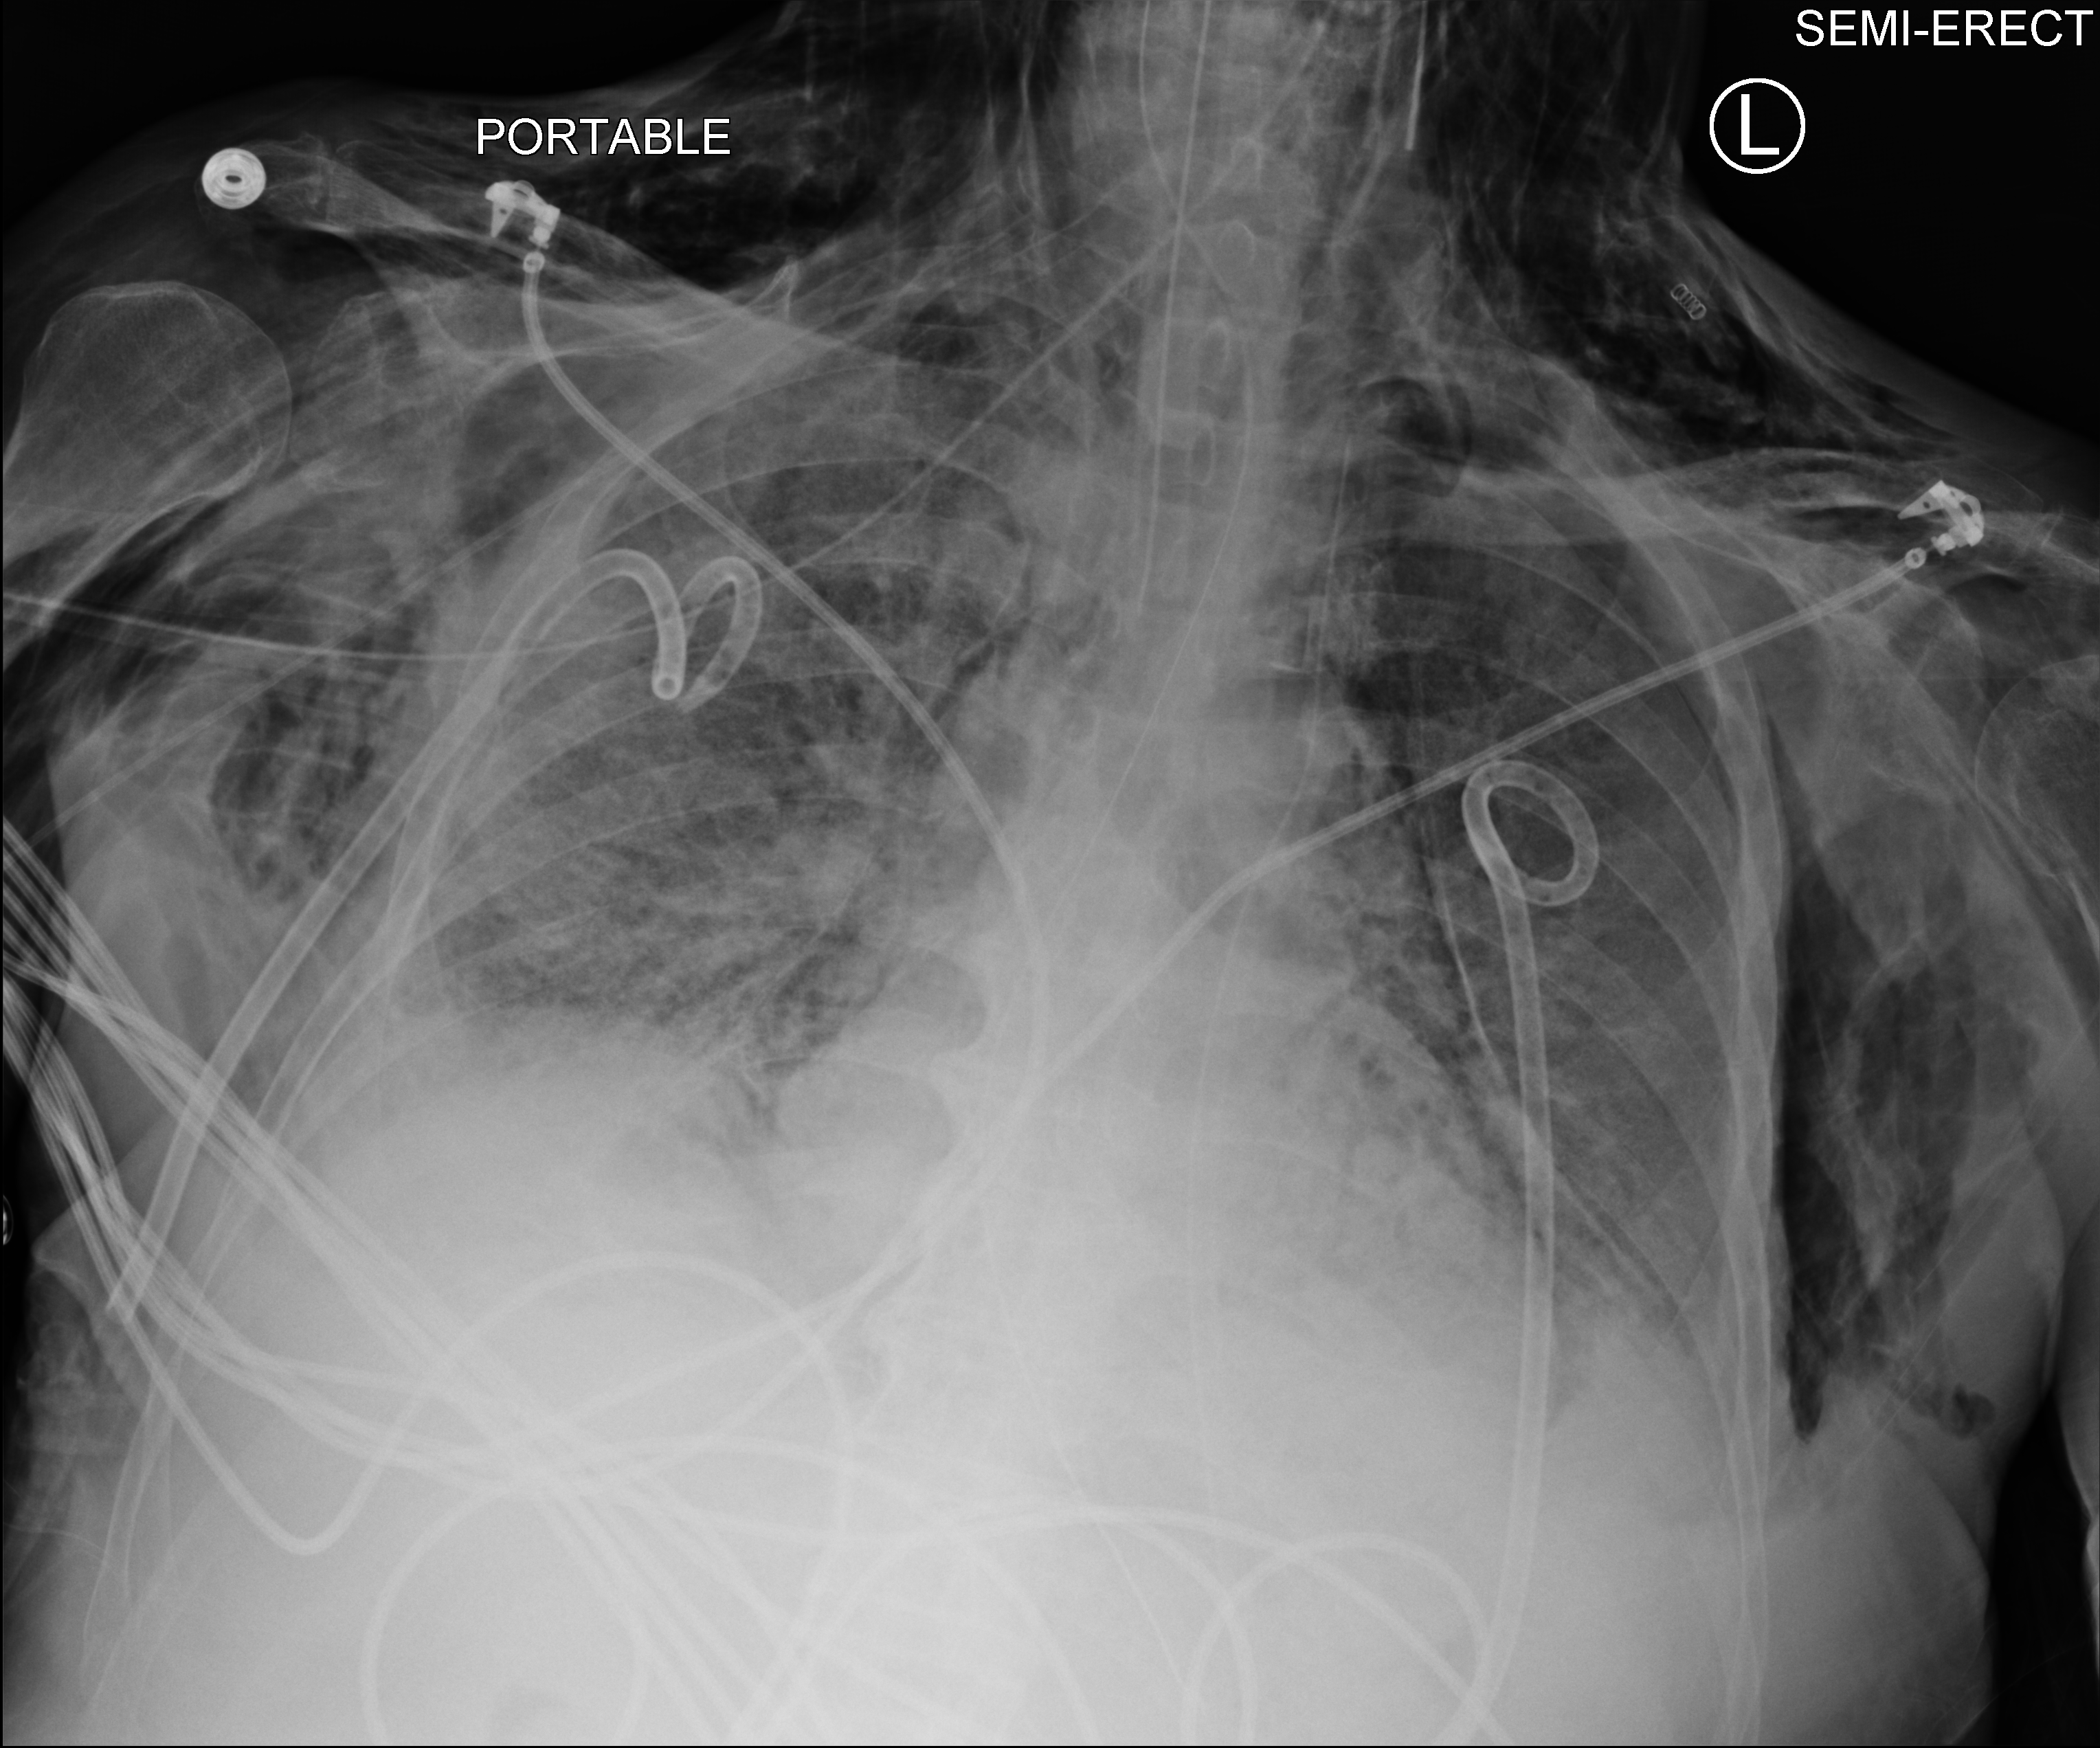
Portable chest radiograph; anteroposterior (AP) projection. Patient hospitalised with COVID-19; male, aged 75–90 years.
From the hospital-stay record, not from the radiograph (when in the stay this image was taken is not recorded): mechanically ventilated during this hospital stay: yes; admitted to intensive care during this hospital stay: yes; length of hospital stay: 30 days.